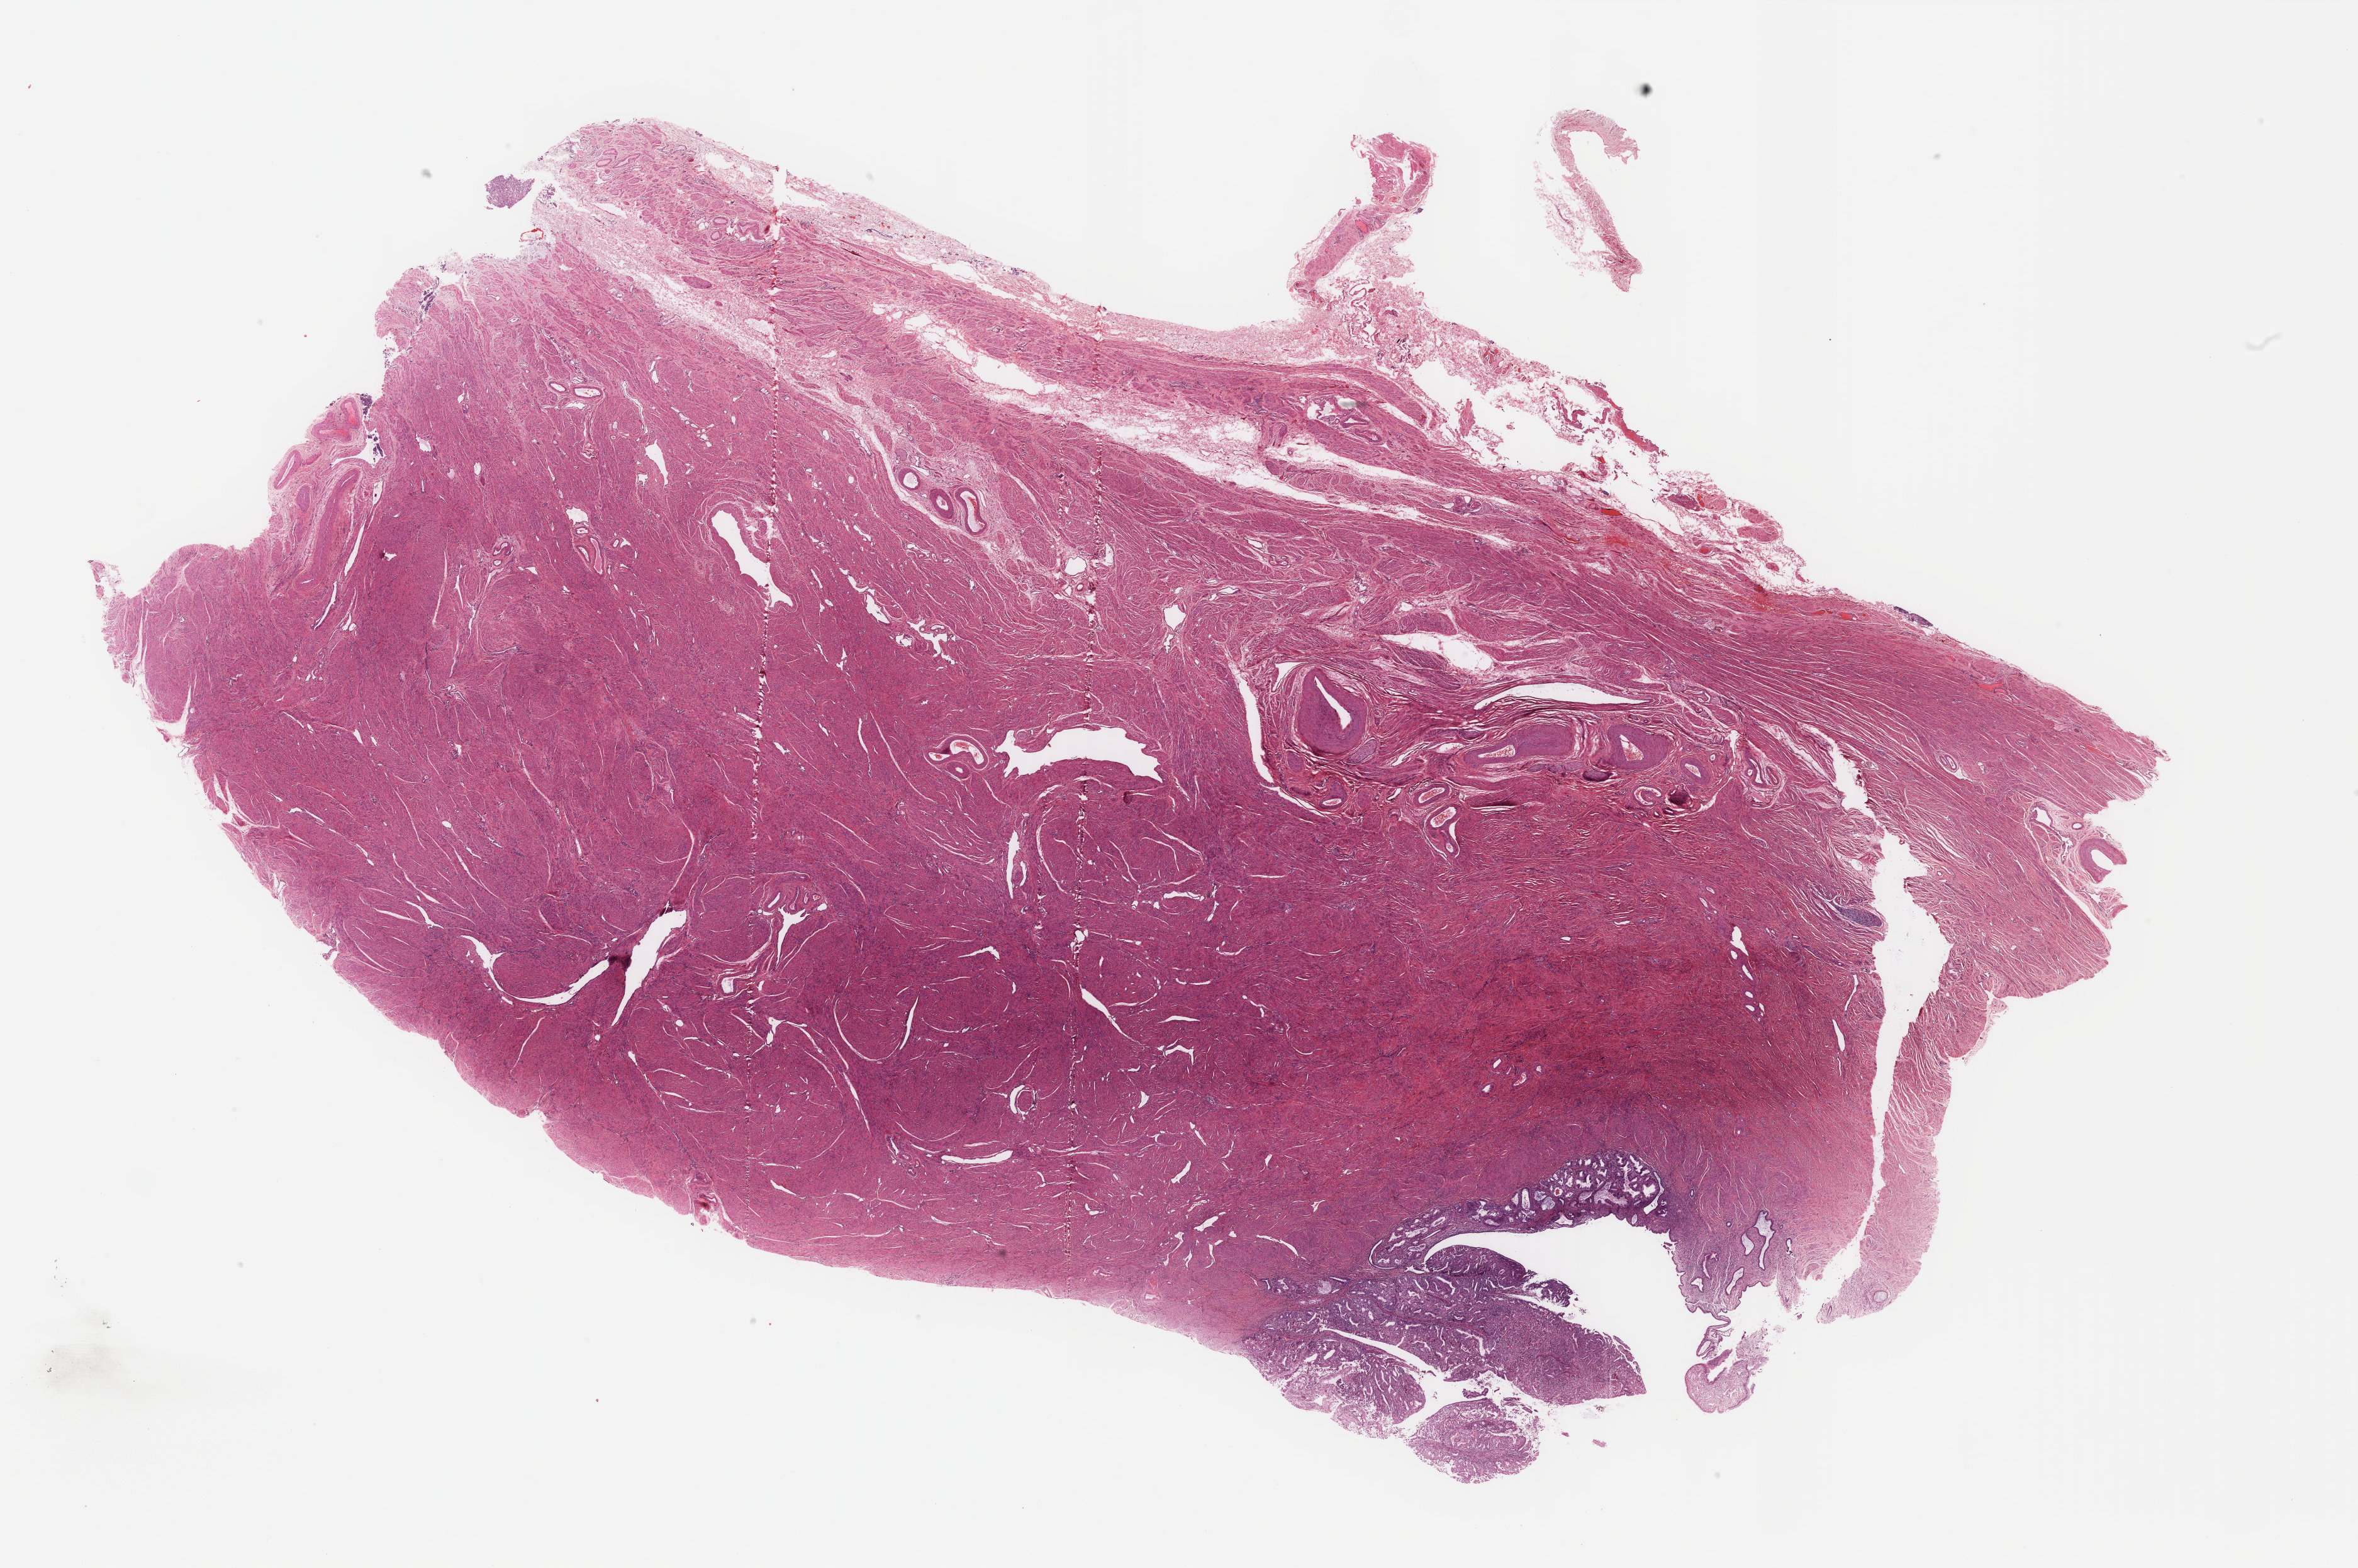
Digitized H&E tissue section (whole slide) — shown as a low-resolution overview of the whole scanned area (about 29.7 x 19.8 mm, slide scanned at 40x). Formalin-fixed paraffin-embedded (FFPE) diagnostic section. Primary tumour sample from the uterus. Female, age 44 years at initial diagnosis. Histologic grade: G2 (moderately differentiated).
- lymph nodes positive (case pathology): 0 of 4 examined
- pathologic diagnosis: Endometrioid adenocarcinoma, NOS (endometrium)
- FIGO stage: IA